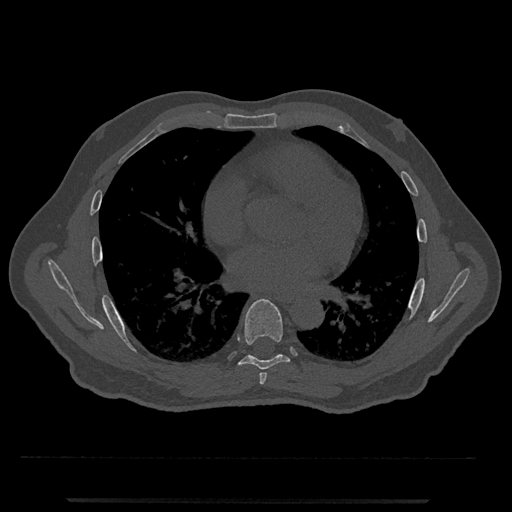
CT including the spine, one axial slice. Reconstruction kernel Br40s/3. 120 kVp. Bone window (W 1800 / L 400 HU). 0.5 mm slice thickness. 512 × 512 image matrix. Patient: male, 63 years. Case-level facts recorded for this patient, not image findings: primary cancer: prostate.
Annotated regions visible in this slice (semi-automatically segmented with operator editing):
- T6 vertebra: bounding box [x1, y1, x2, y2] px = [259, 372, 267, 385]
- T7 vertebra: [236, 299, 290, 370]